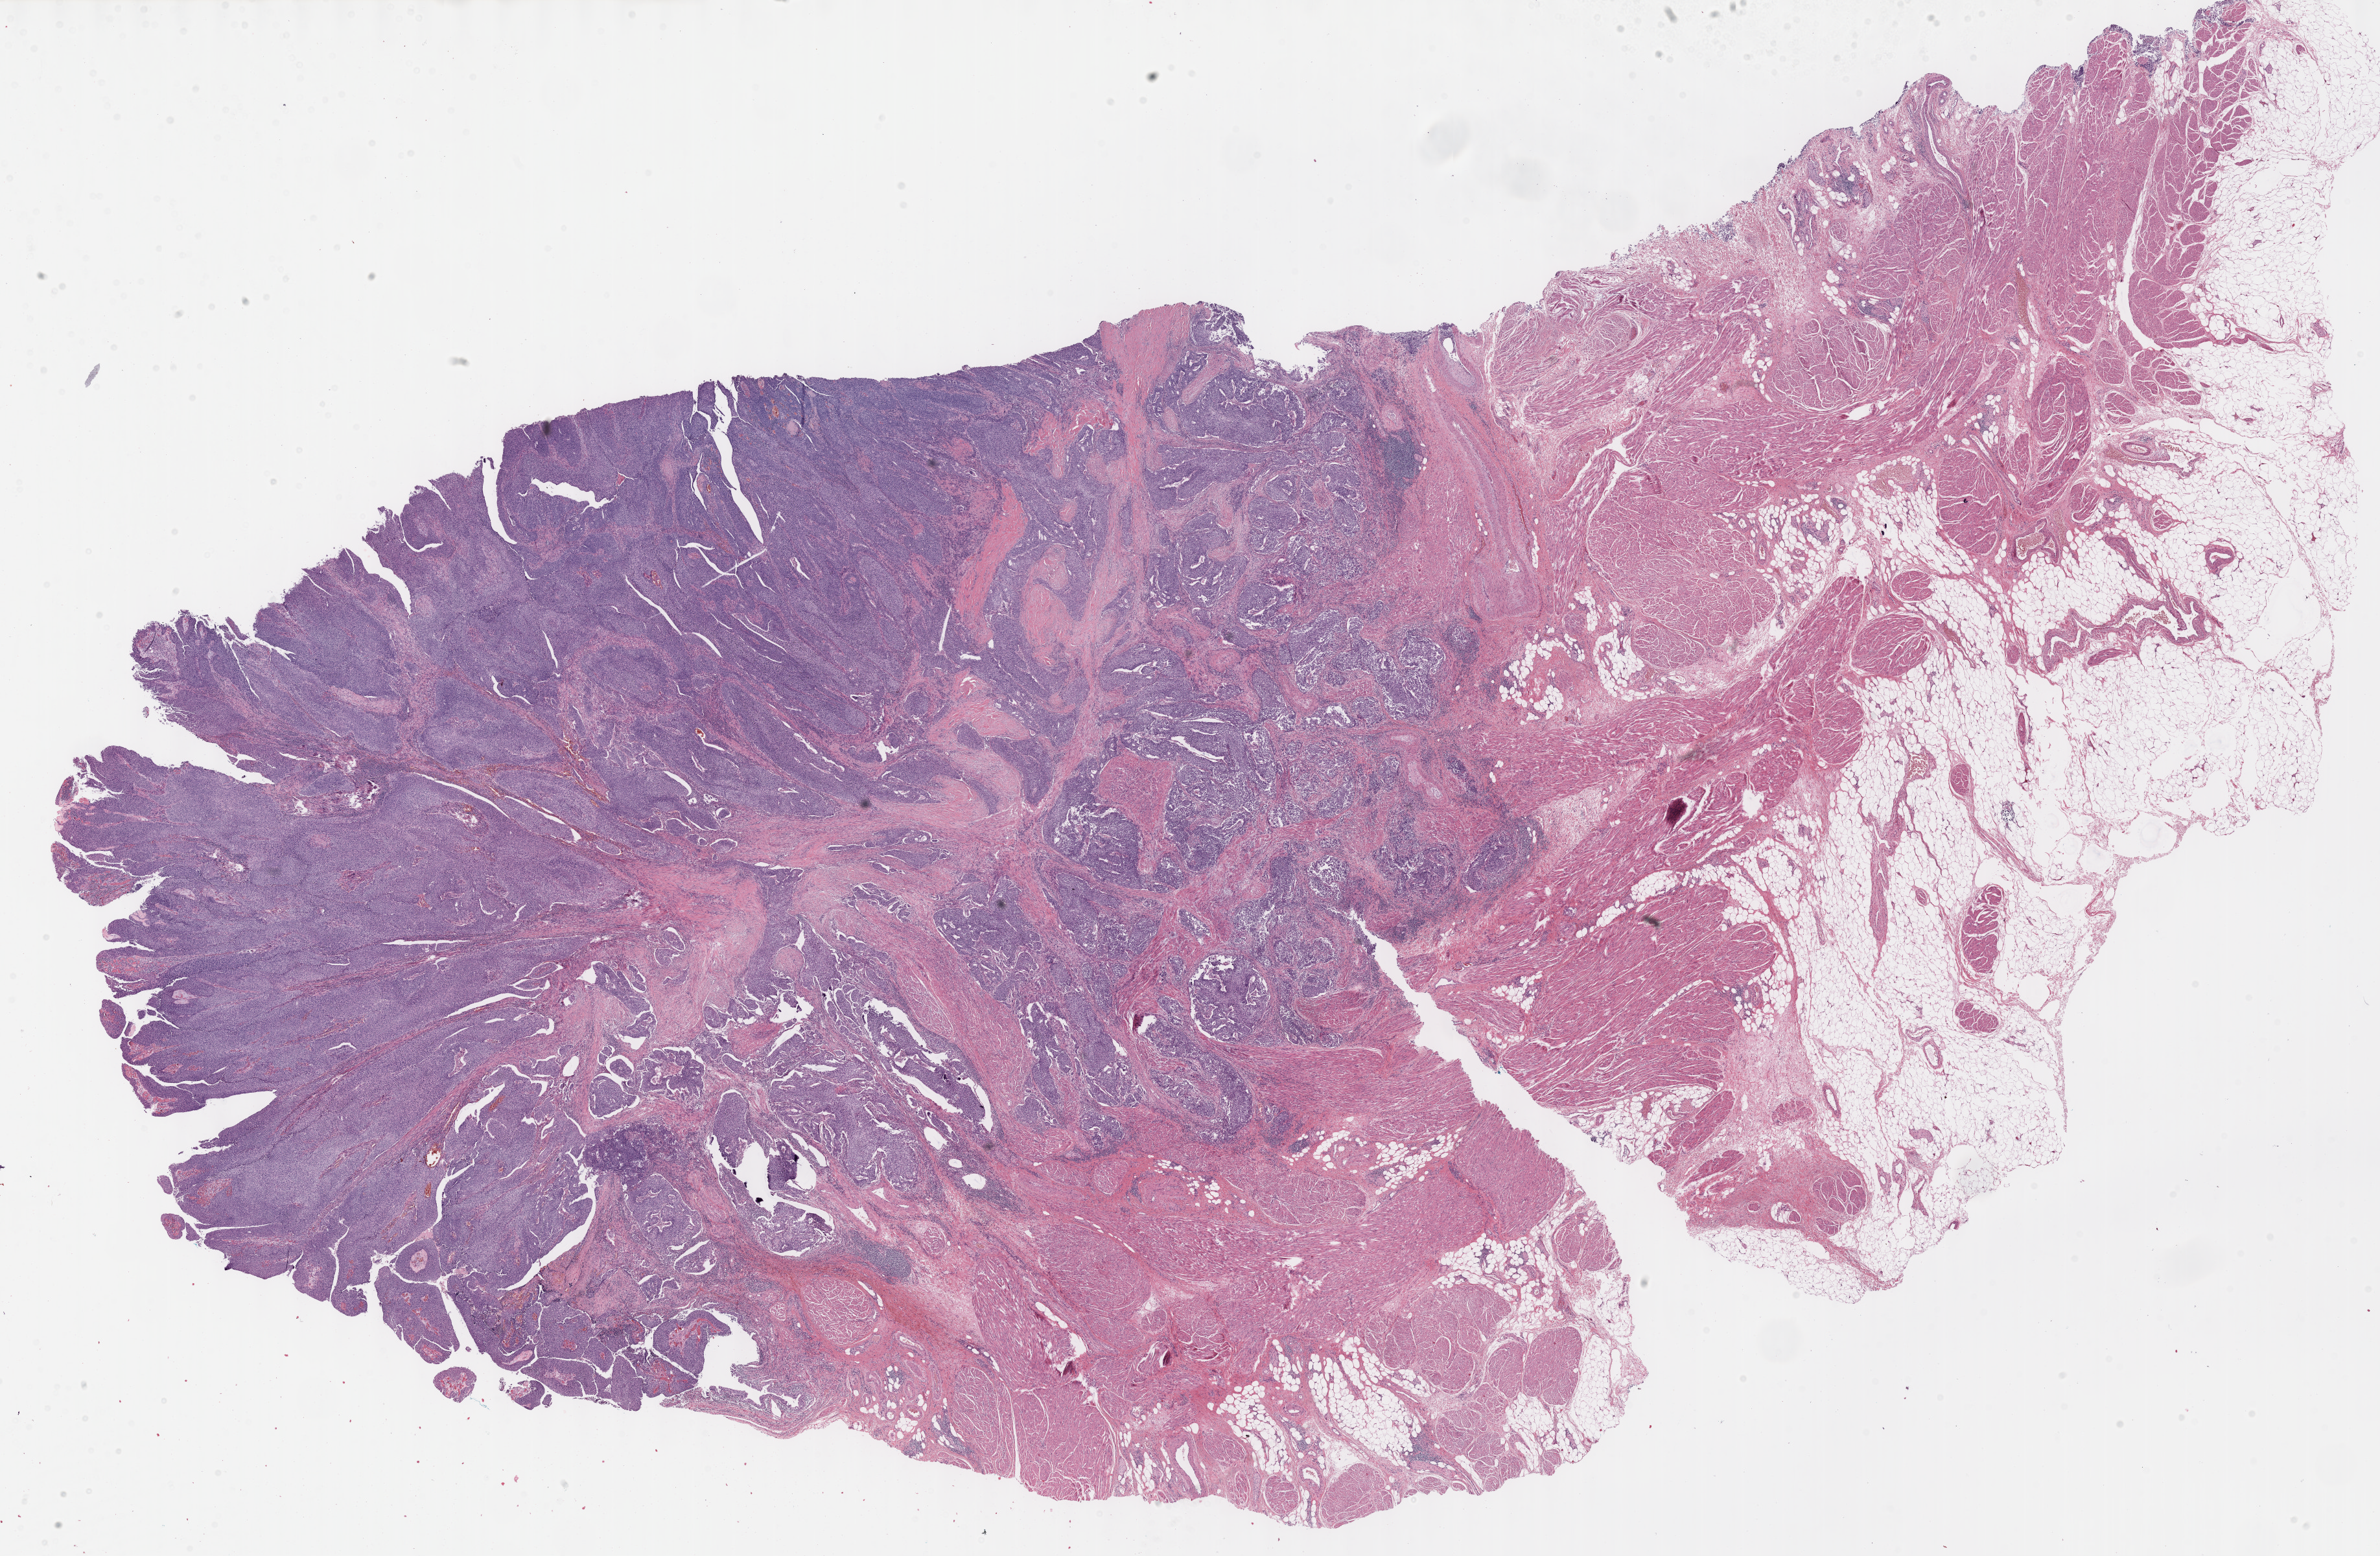
H&E whole-slide image, low-resolution overview of the scanned area, about 29.7 x 19.4 mm. FFPE section. Sample: primary tumour, bladder. Patient: male, age at initial diagnosis 64 years.
Pathologic diagnosis: Papillary transitional cell carcinoma (lateral wall of bladder).